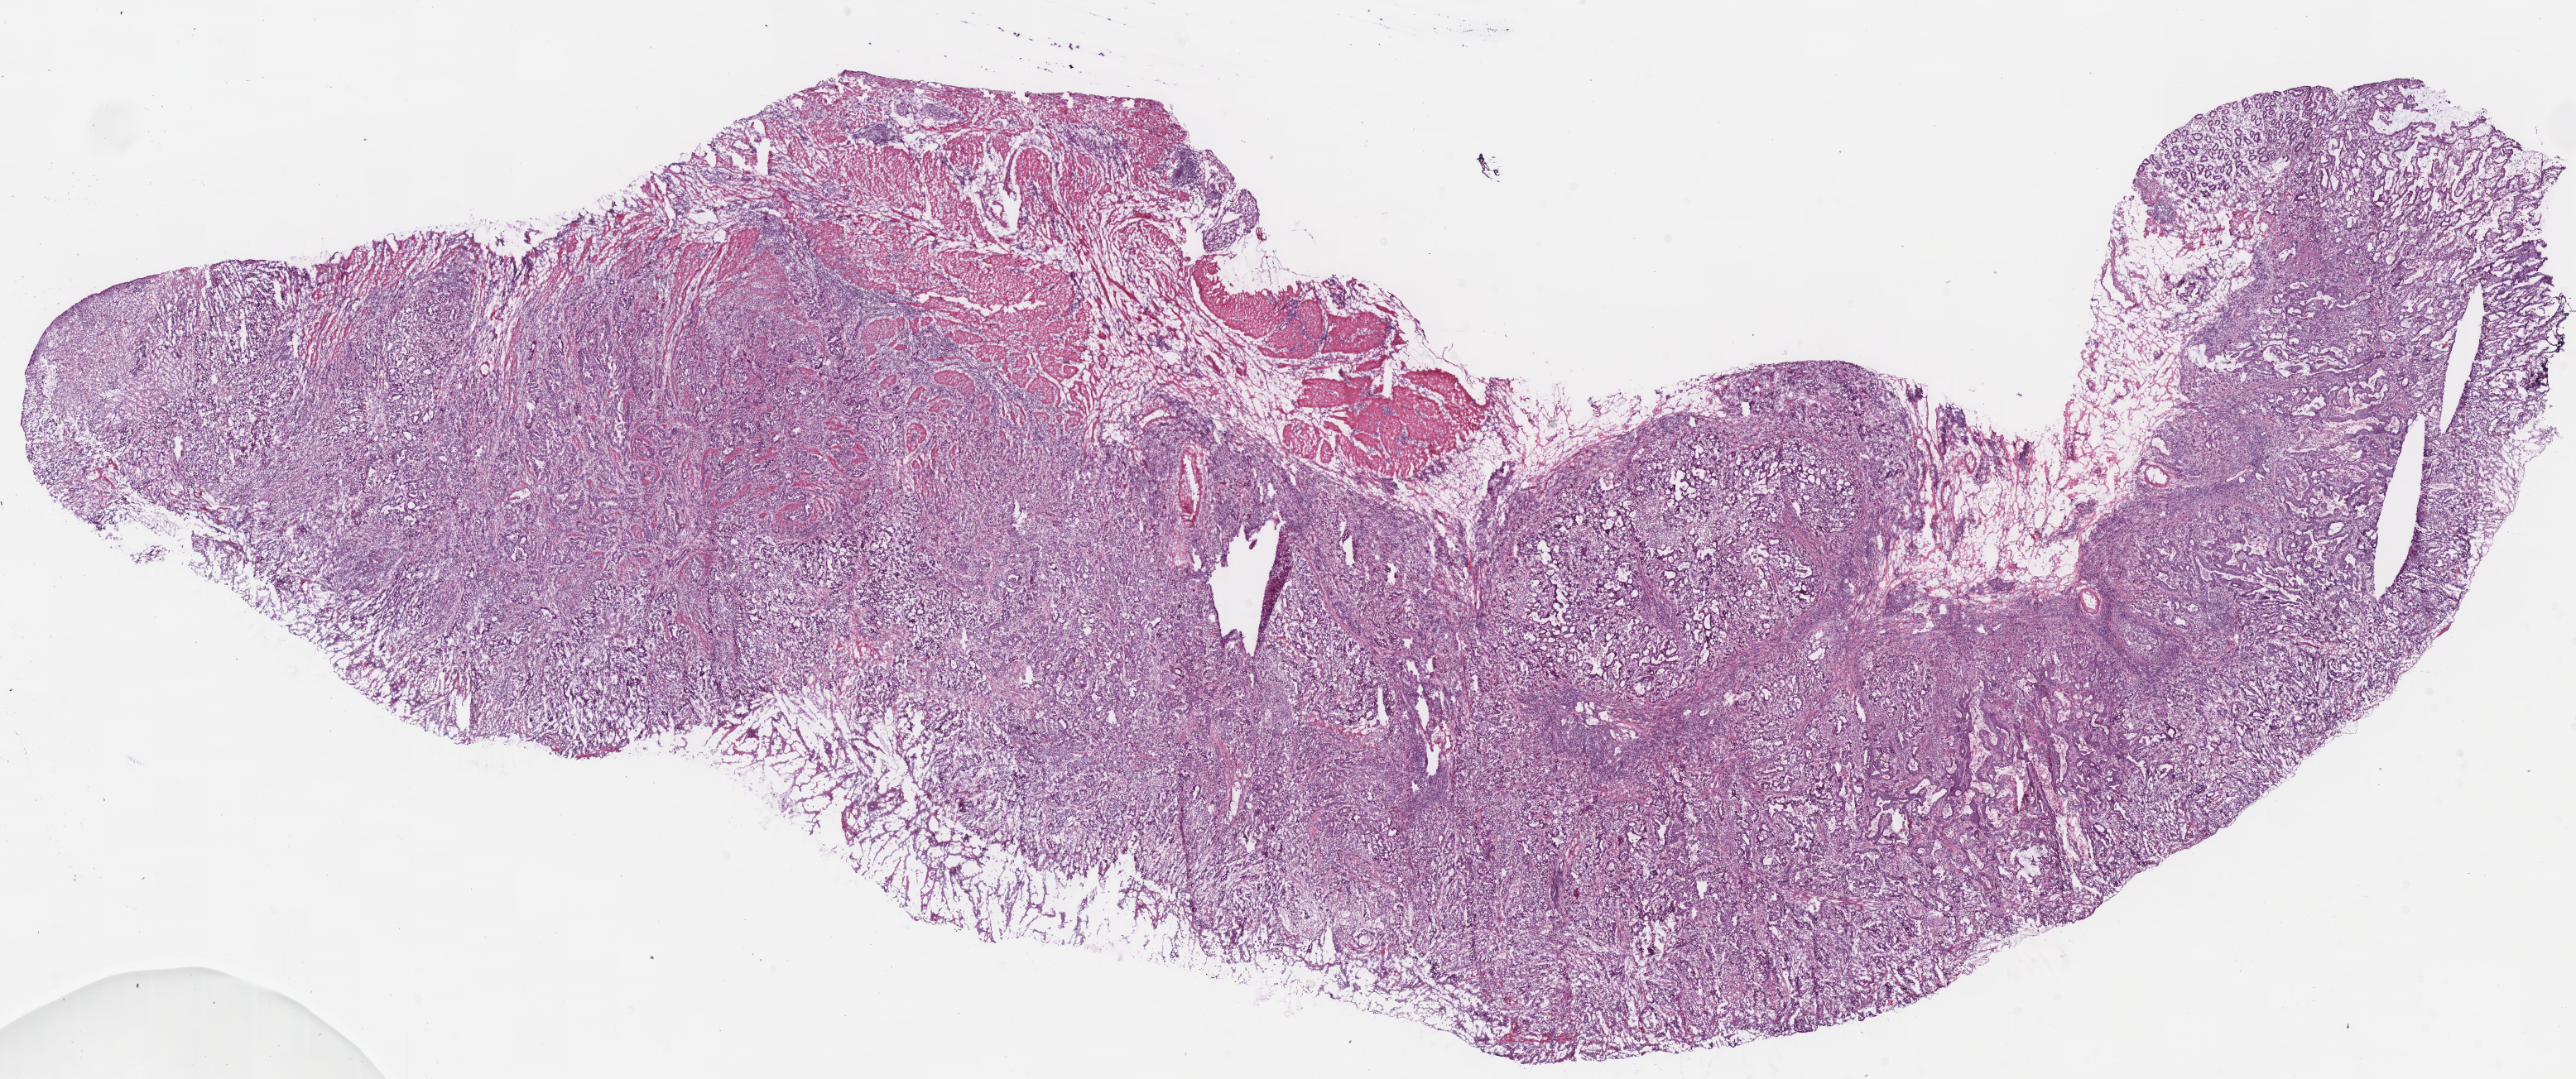
Digitized H&E tissue section (whole slide) — shown as a low-resolution overview of the whole scanned area (about 24.5 x 10.3 mm); frozen section from the bottom of the tissue portion; stomach, primary tumour sample. Male patient; age at initial diagnosis 79 years. Histologic grade: G3 (poorly differentiated). Pathologist review of this section (percent, as recorded): tumour cells 78%, tumour nuclei 75%, normal cells 2%, stromal cells 20%, necrosis 0%.
* AJCC pathologic stage: IIIC
* diagnosis: Adenocarcinoma, NOS (gastric antrum)